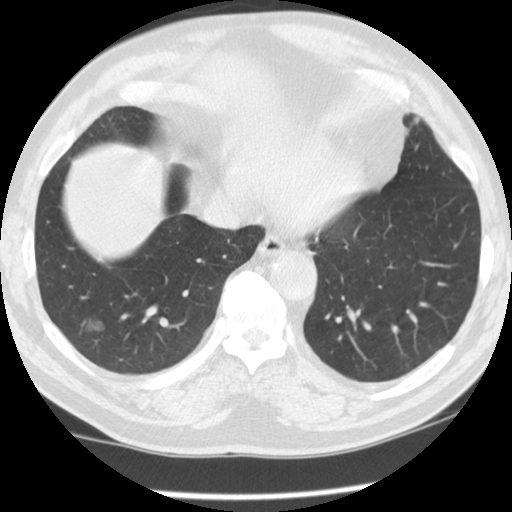
Low-dose screening chest CT, one axial slice; position 30 of 115 along the scan axis; 120 kVp; lung window (W 1500 / L -600 HU); 2.5 mm slice thickness; 512 × 512 image matrix.
Outlined on this slice (manually delineated by an expert):
- lesion 1 (tumor, lower lobe of right lung): bounding box (x1, y1, x2, y2) in pixels: (88, 321, 101, 330)